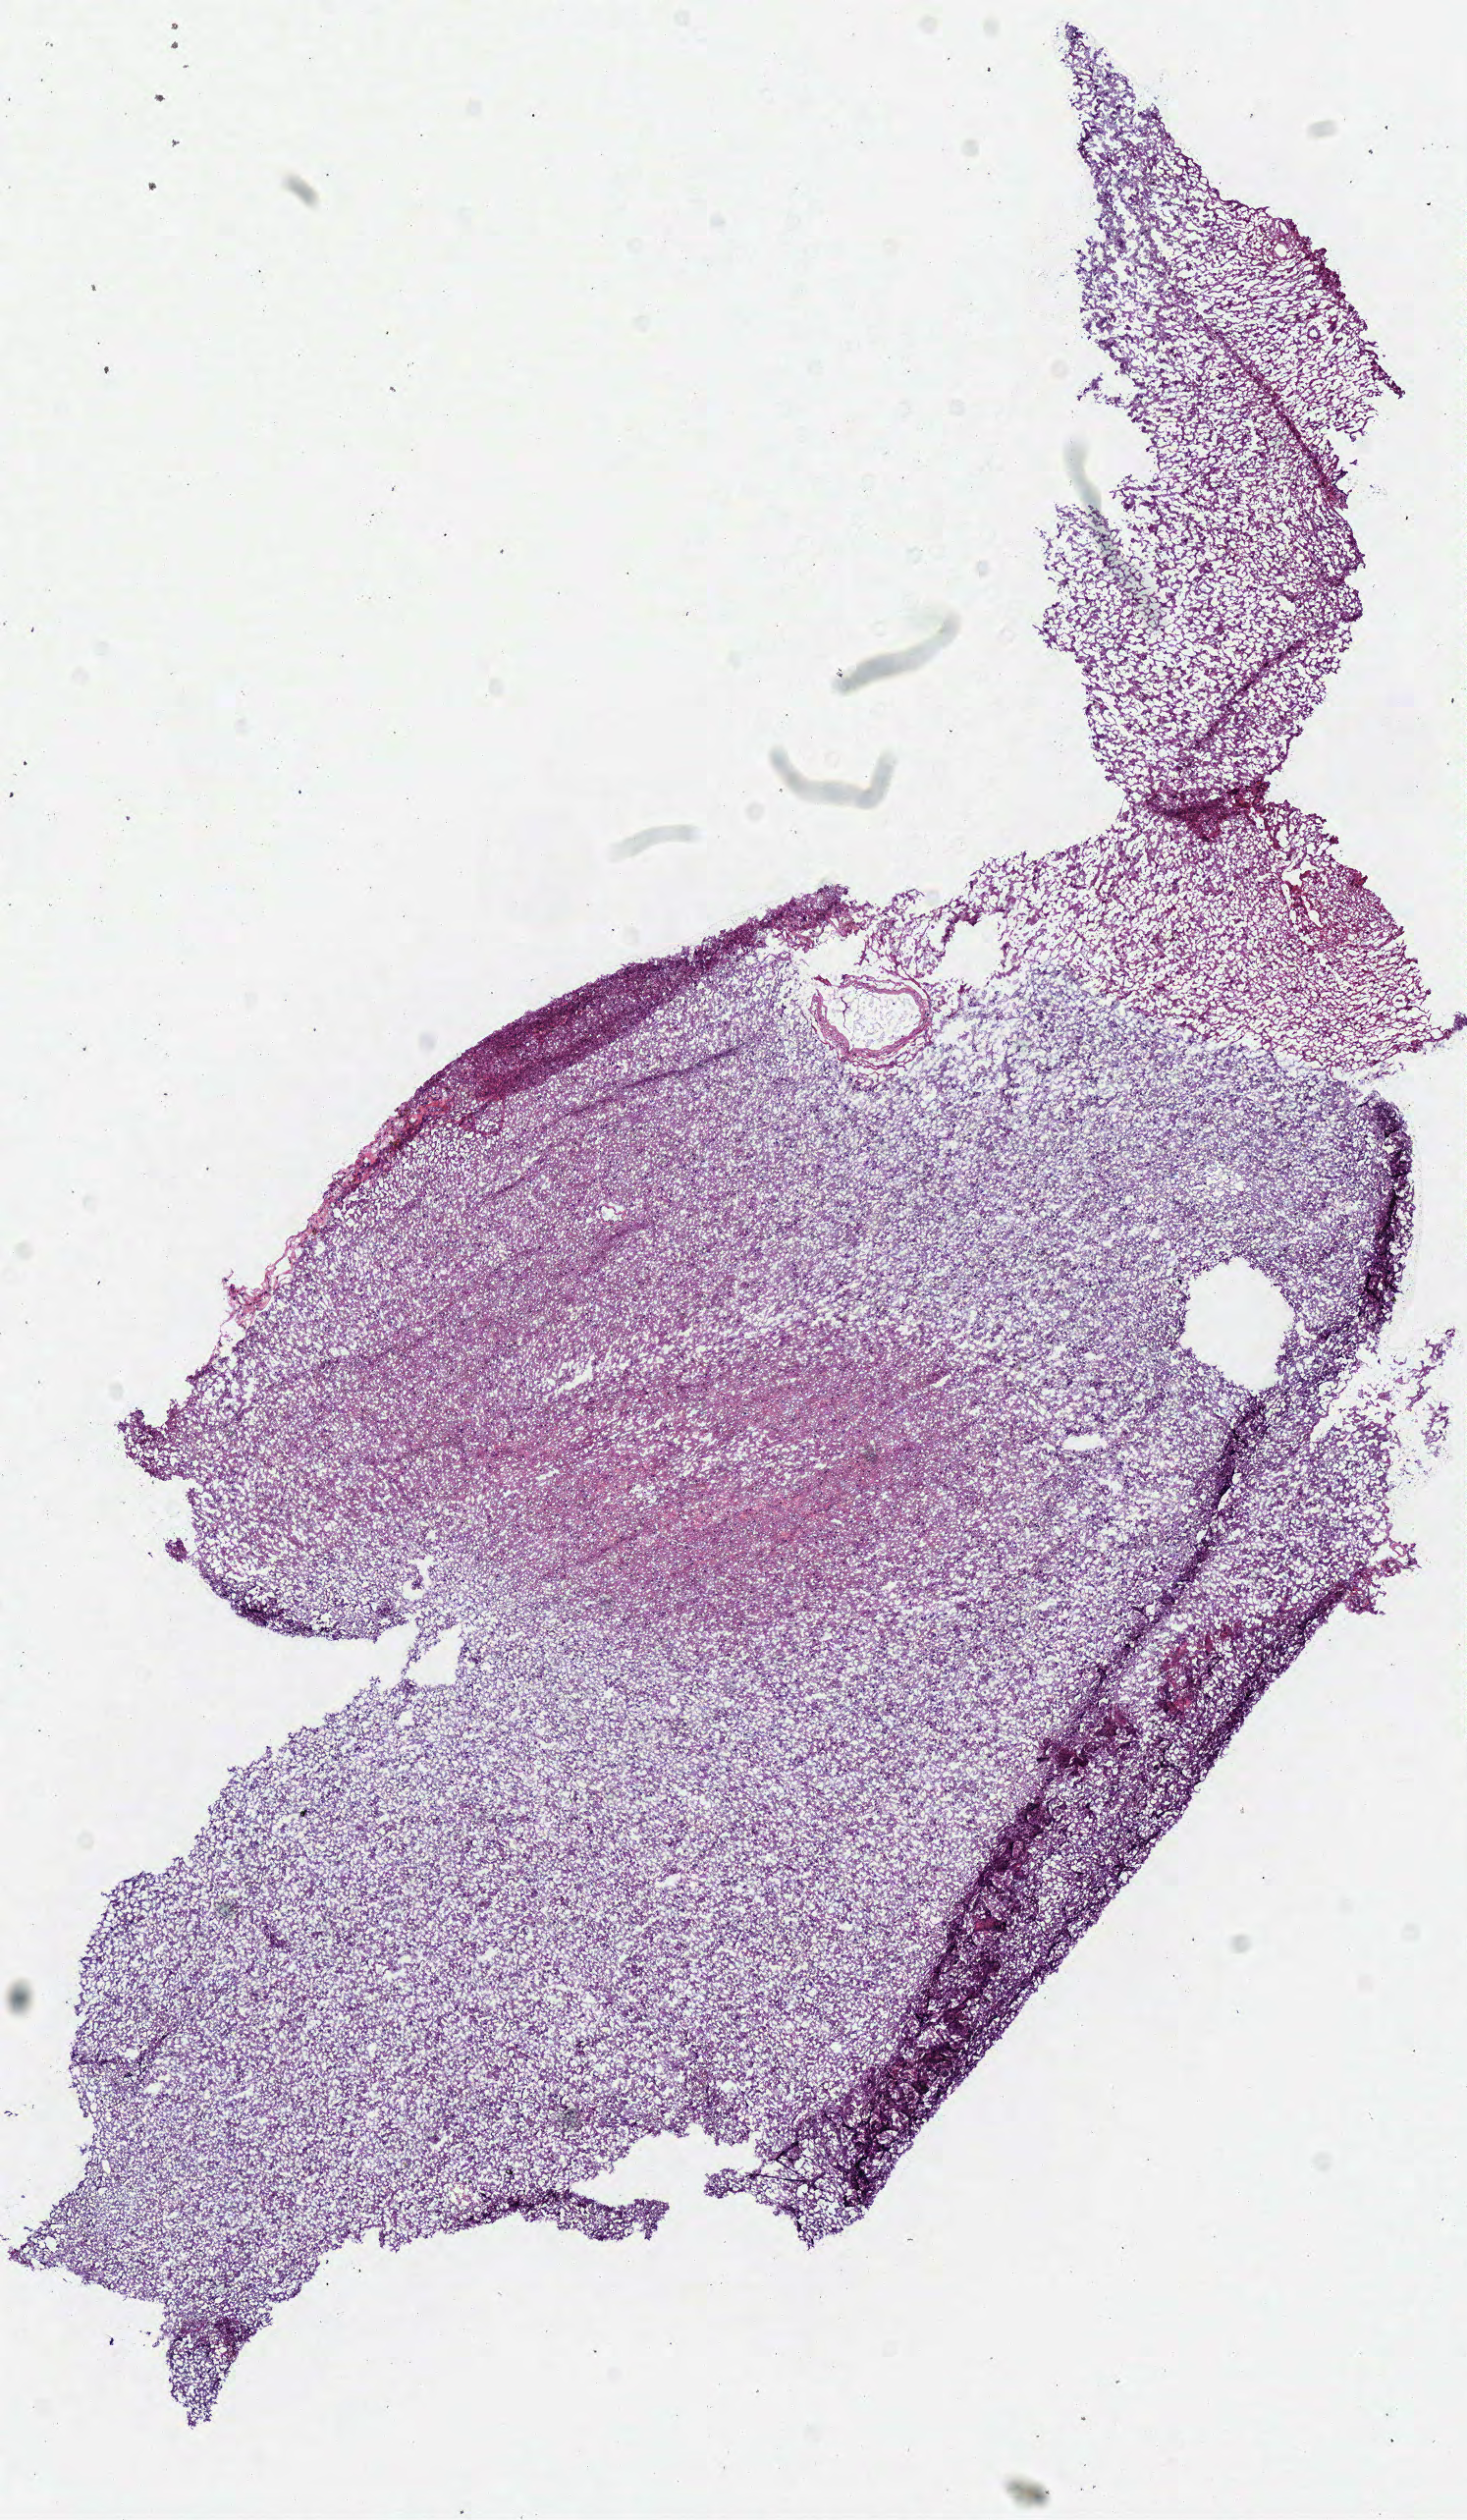
H&E-stained whole-slide image, a low-resolution overview of the entire scanned area, about 5.9 x 10.1 mm (slide scanned at 40x); frozen section from the bottom of the tissue portion; brain, primary tumour sample. Male, age 54 years at initial diagnosis. Histologic grade: G3 (poorly differentiated). Slide review estimates, as recorded: tumour cells 100%, tumour nuclei 60%, normal cells 0%, stromal cells 0%, necrosis 0%.
Histologic diagnosis: Oligodendroglioma, anaplastic (cerebrum).